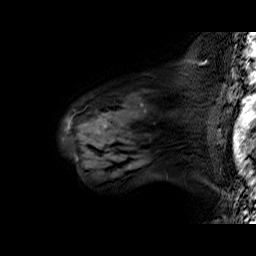
Breast MRI (dynamic contrast-enhanced), one sagittal slice; position 46 of 60 along the scan axis; dynamic contrast-enhanced series, time point 2 of 6 at this slice position (early post-contrast); 1.5 T; TE 6.4 ms, TR 32.9 ms; 4 mm slice thickness; 256 × 256 image matrix, field of view 200 × 200 mm. Female patient. Case-level facts recorded for this patient, not image findings: setting: breast cancer imaged before/during neoadjuvant chemotherapy; receptor status: HER2-positive.
Structures marked on this image (semi-automatic segmentation, software-assisted and operator-edited):
- analysis volume of interest (the breast-tissue region the enhancement analysis was run in; not a lesion): bounding box [x1, y1, x2, y2] px = [61, 78, 196, 160]
- tumour enhancement mask (voxels above the 100 % enhancement threshold inside the analysis volume of interest): [66, 104, 143, 160]